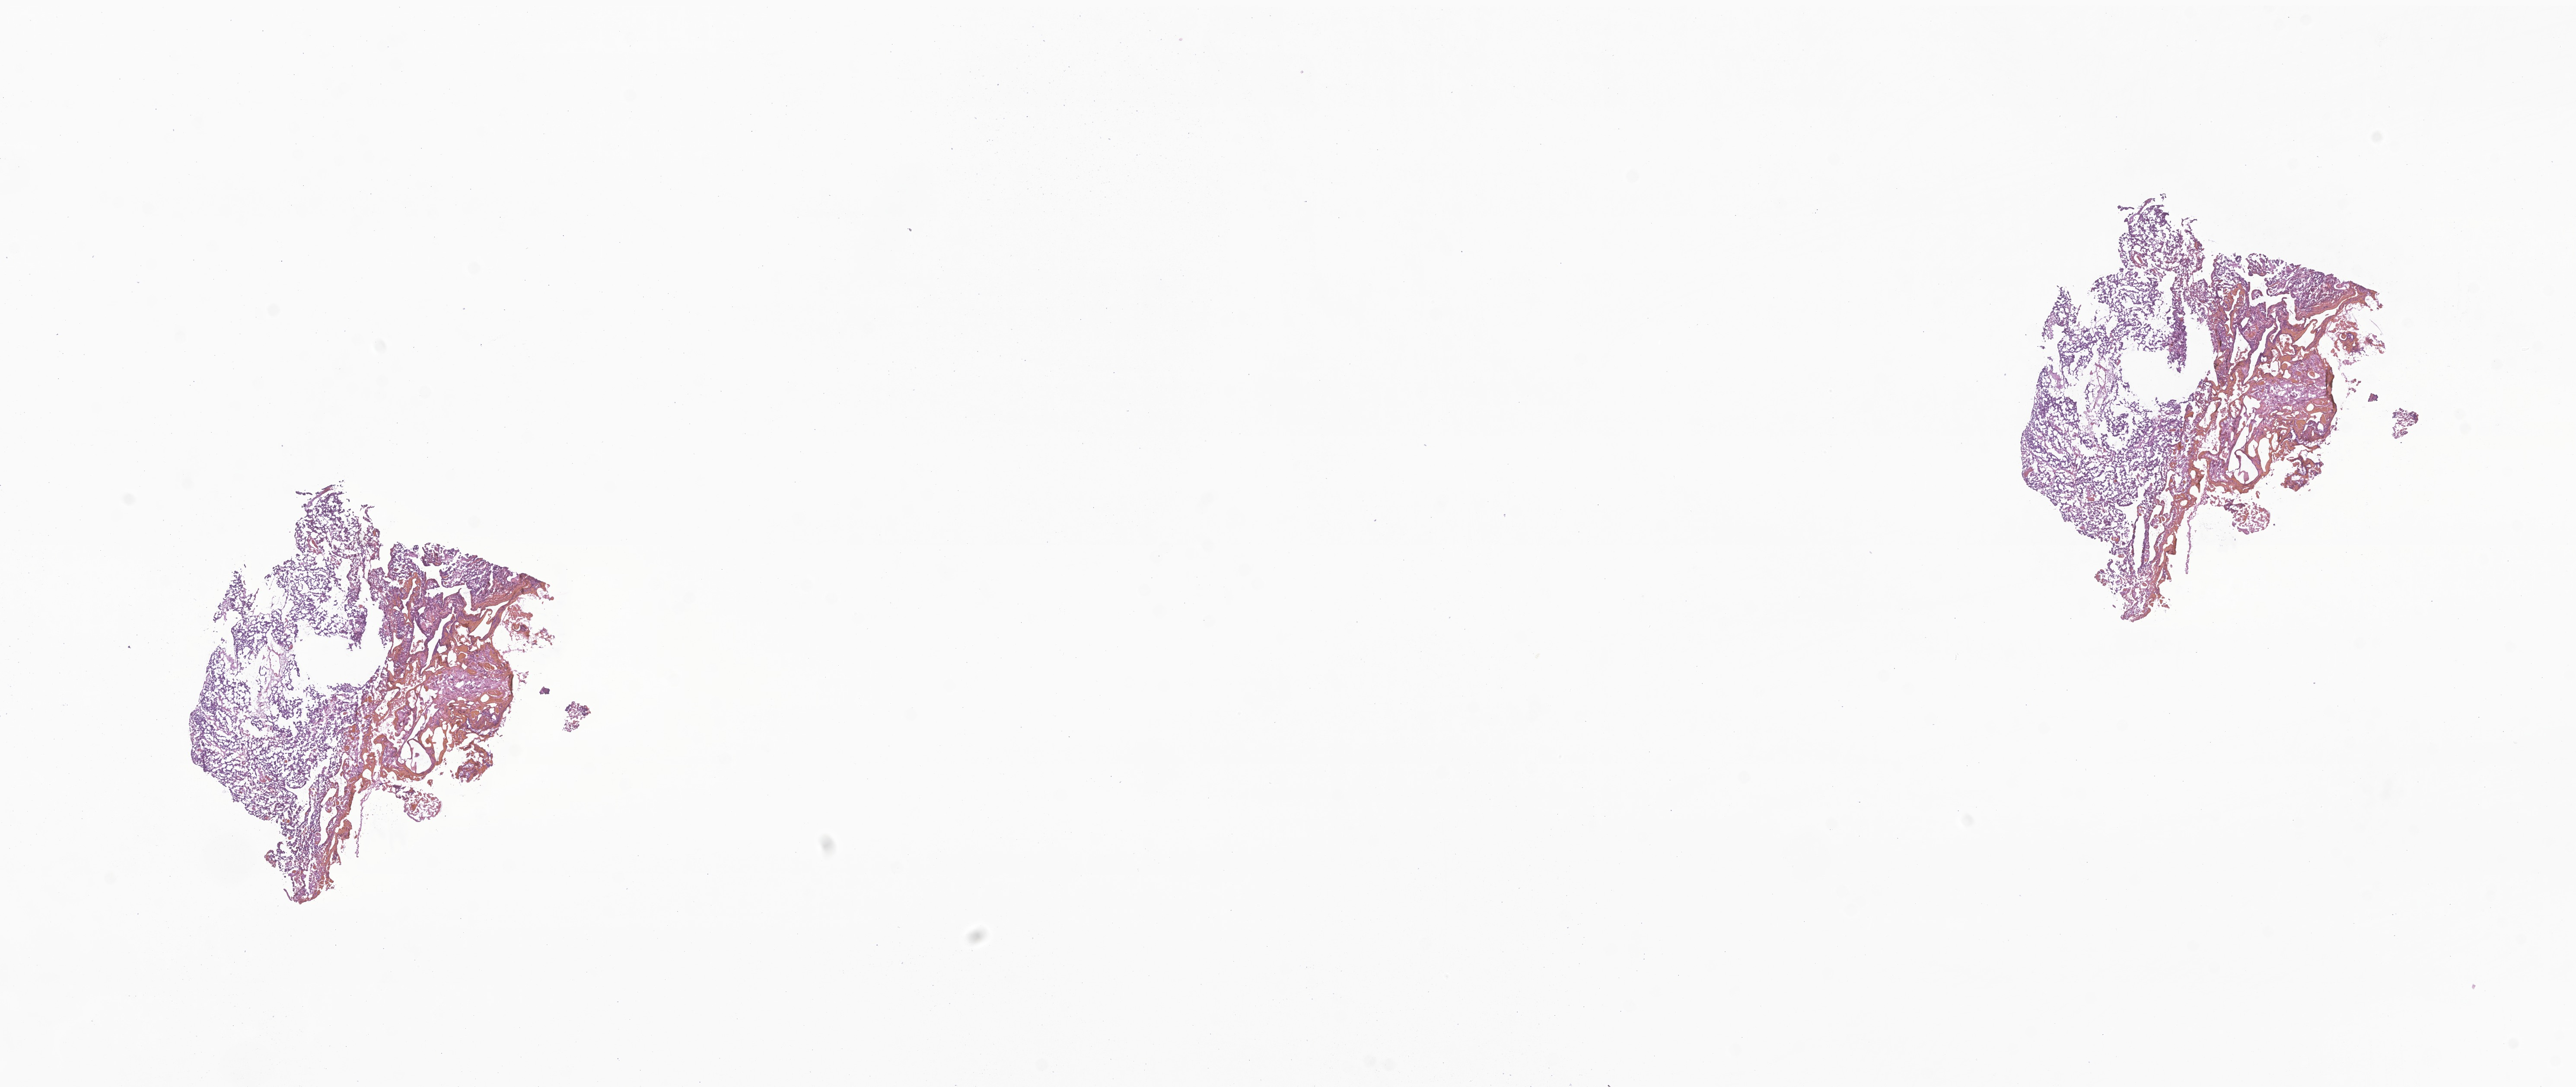
Whole-slide image, haematoxylin and eosin stain of tumor tissue from the brain — whole scanned area (about 25.1 x 10.6 mm) shown as a low-resolution overview; frozen section (OCT-embedded). Patient: female, age 87 months (7 years 3 months).
- recorded diagnosis: Medulloblastoma, NOS